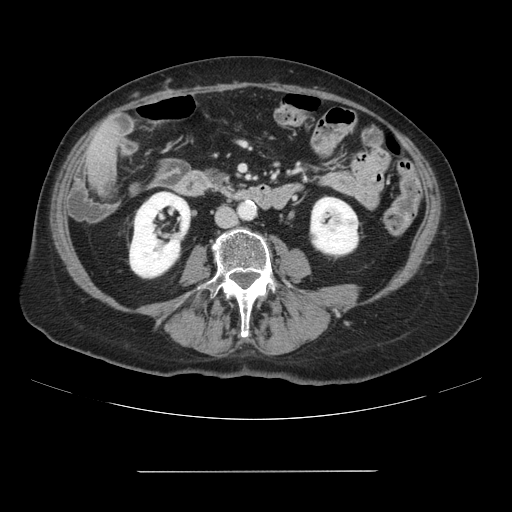
Contrast-enhanced abdominal CT, one axial slice. Slice 8 of 111 in the series (ordered by position). Intravenous contrast given. Soft-tissue window (W 400 / L 40 HU). 2.5 mm slice thickness. 512 × 512 image matrix, field of view 400 × 400 mm. Female patient, age 74 years. Case-level facts recorded for this patient, not image findings: diagnosis: colorectal cancer liver metastases, imaged before liver resection; multiple liver metastases: yes; largest metastasis: 1.1 cm.
Annotated regions visible in this slice (outlined manually by an expert reader):
- liver: bounding box (x1, y1, x2, y2) in pixels: (88, 122, 119, 185)